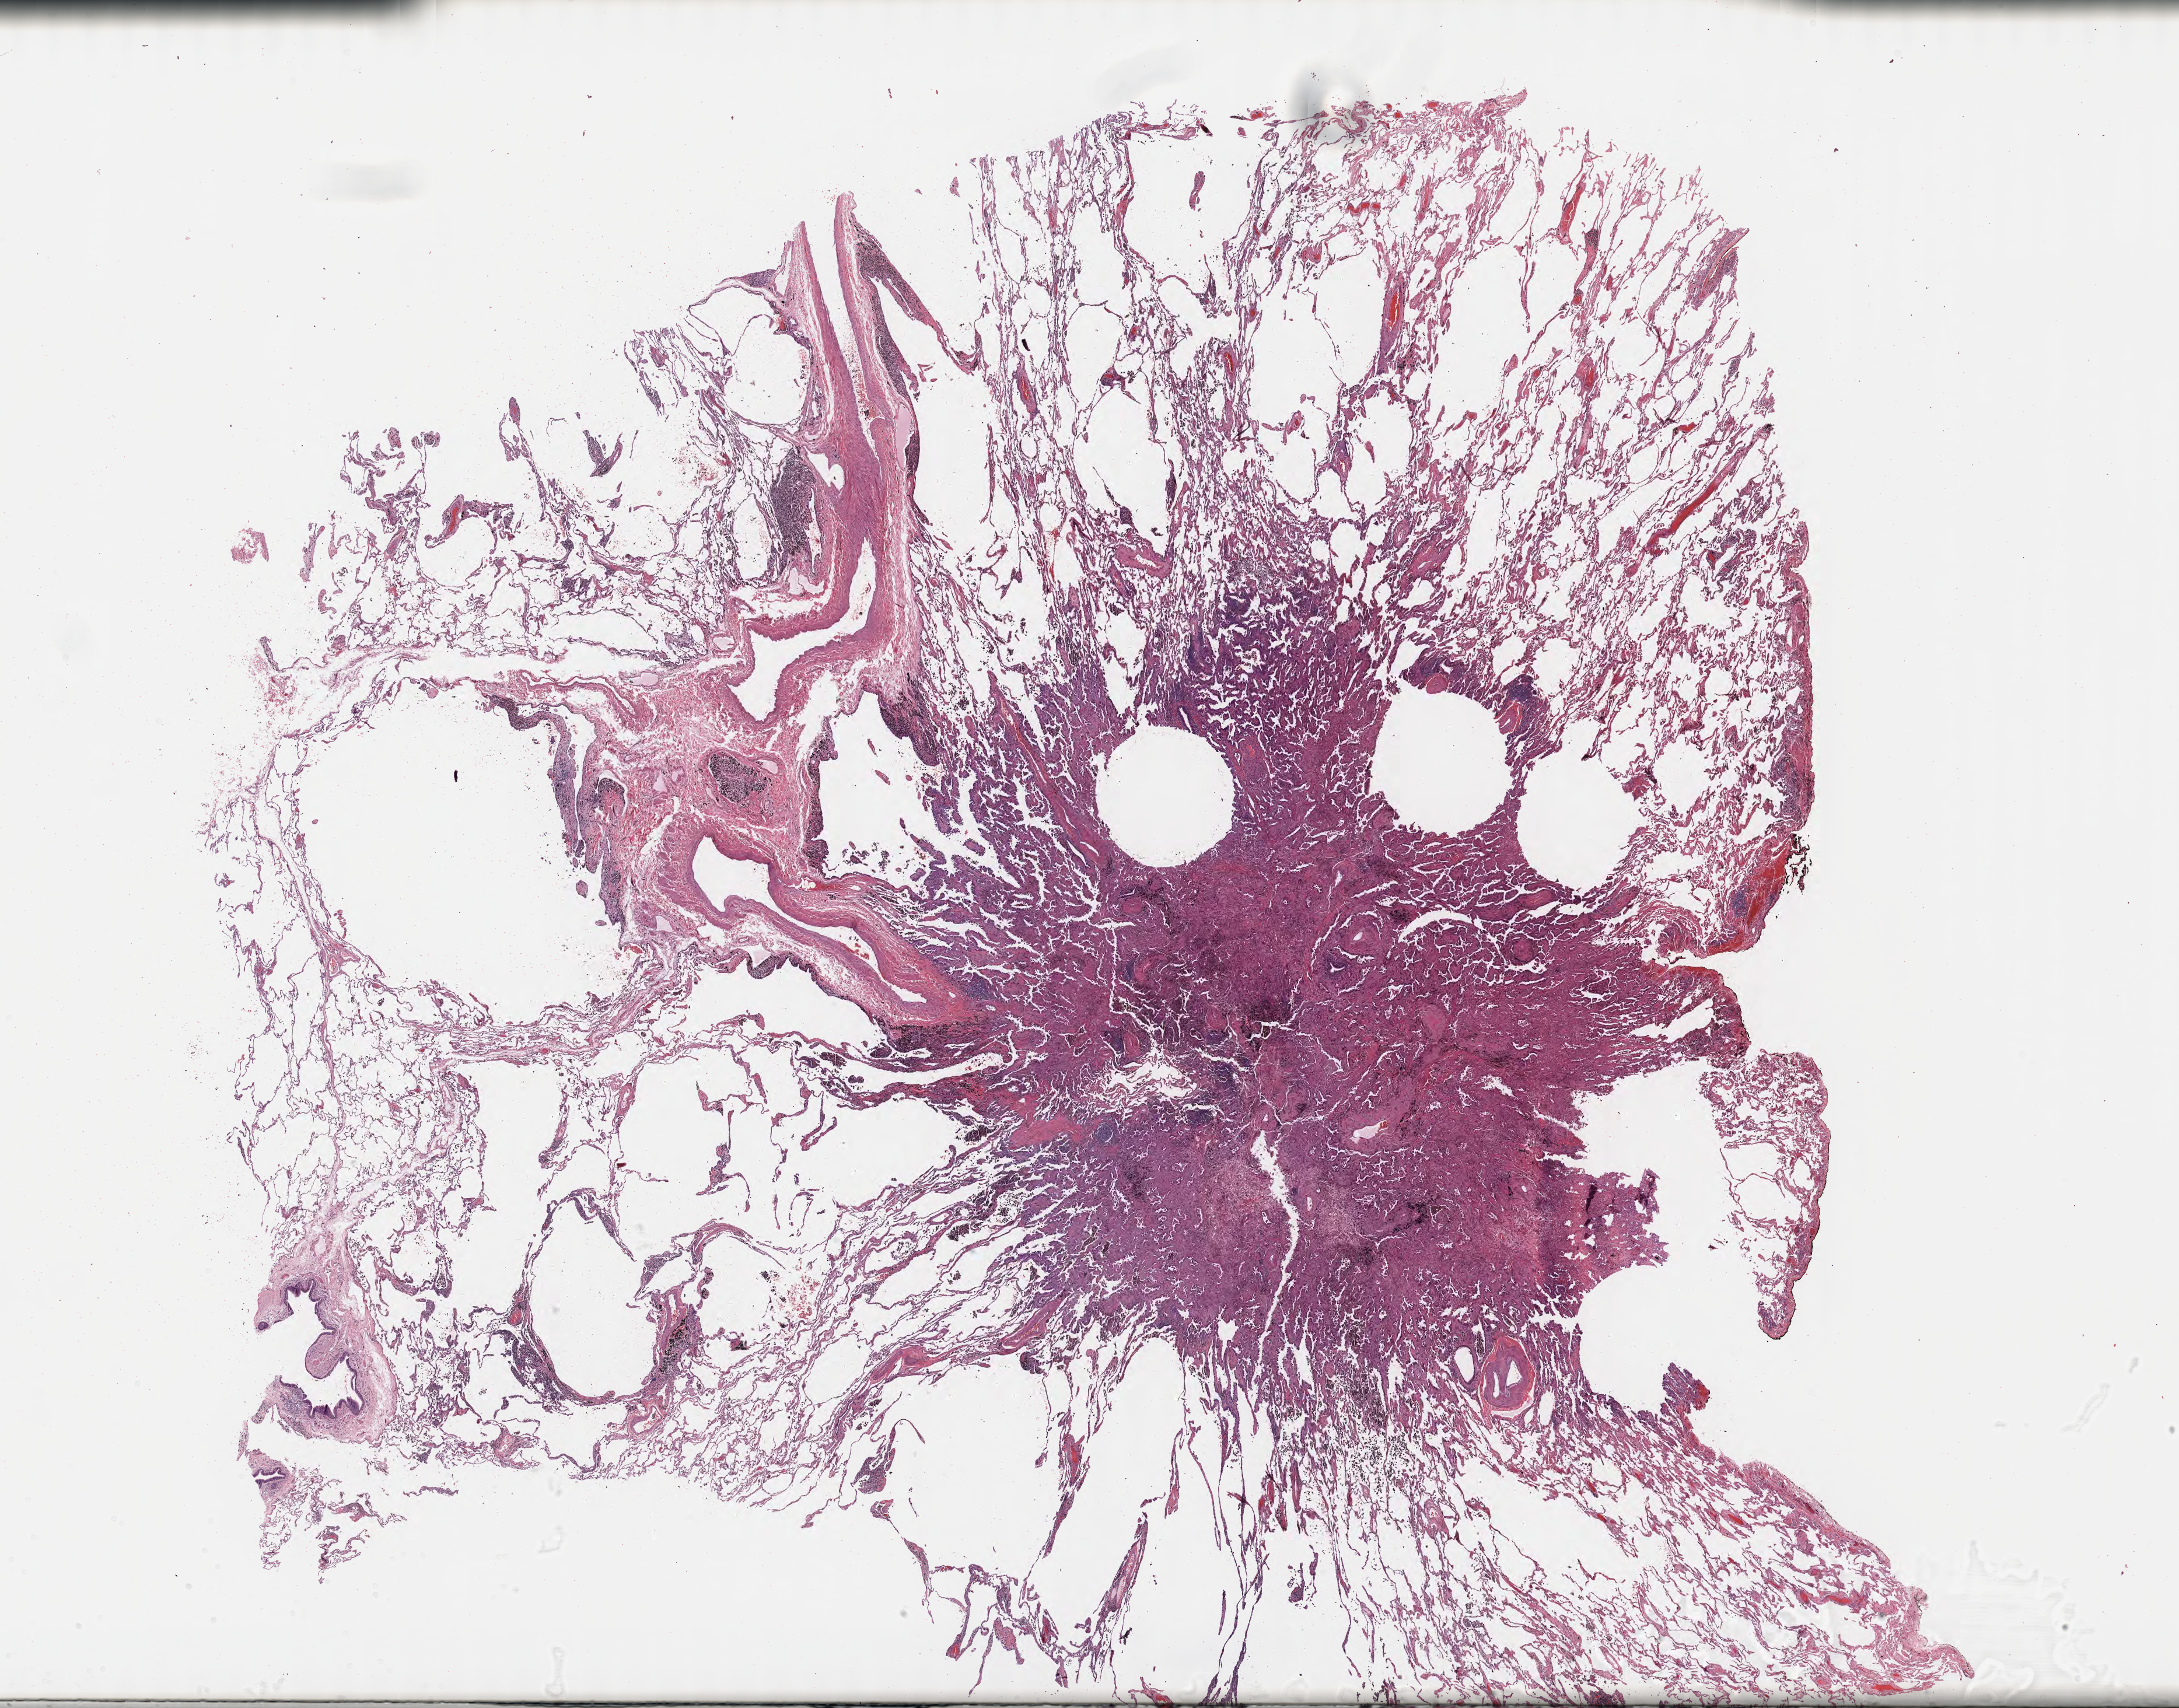
H&E whole-slide image, shown as a low-resolution overview of the whole scanned area (about 30.2 x 23.7 mm), tumor tissue, anatomic site: lung. Male patient.
Diagnosis: Mucinous adenocarcinoma.